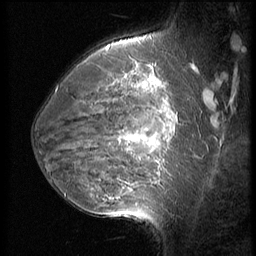
Breast MRI (dynamic contrast-enhanced), one sagittal slice. Position 40 of 56 along the scan axis. 3 images stored at this slice position (order not interpretable as contrast timing). 1.5 T. TE 4.2 ms, TR 9 ms. 2.5 mm slice thickness. 256 × 256 image matrix, field of view 180 × 180 mm. Patient: female, 35 years. Case-level facts recorded for this patient, not image findings: setting: breast cancer imaged before/during neoadjuvant chemotherapy; receptor status: HR-positive, HER2-negative.
Outlined on this slice (semi-automatic segmentation, software-assisted and operator-edited):
- analysis volume of interest (the breast-tissue region the enhancement analysis was run in; not a lesion): bounding box <63,60,190,218> (left, top, right, bottom; pixels)
- tumour enhancement mask (voxels above the 140 % enhancement threshold inside the analysis volume of interest): <104,84,172,199>